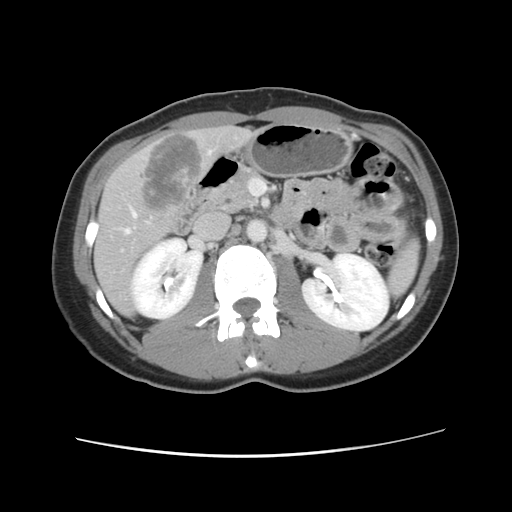
Contrast-enhanced abdominal CT, one axial slice; 120 kVp; intravenous contrast given; soft-tissue window (W 400 / L 40 HU); 2.5 mm slice thickness; 512 × 512 image matrix, field of view 339 × 339 mm. Female patient, age 33 years. Case-level facts recorded for this patient, not image findings: diagnosis: colorectal cancer liver metastases, imaged before liver resection; multiple liver metastases: yes; largest metastasis: 4.5 cm; chemotherapy before resection: no.
Structures marked on this image (outlined manually by an expert reader):
- hepatic veins: bounding box [x1, y1, x2, y2] px = [125, 151, 212, 234]
- liver: [95, 127, 254, 314]
- planned liver remnant (the part of the liver to remain after resection): [94, 132, 254, 314]
- liver metastasis: [137, 133, 205, 212]